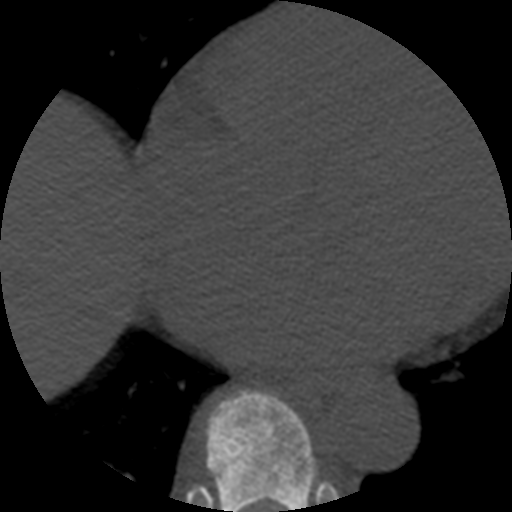
CT including the spine, one axial slice; position 317 of 508 along the scan axis; reconstruction kernel STANDARD; 120 kVp; bone window (W 1800 / L 400 HU); 512 × 512 image matrix, field of view 160 × 160 mm. Patient age 57 years. From the clinical record (not read from this slice): primary cancer: prostate.
Outlined on this slice (semi-automatically segmented with operator editing):
- T8 vertebra: bounding box <206,391,317,512> (left, top, right, bottom; pixels)